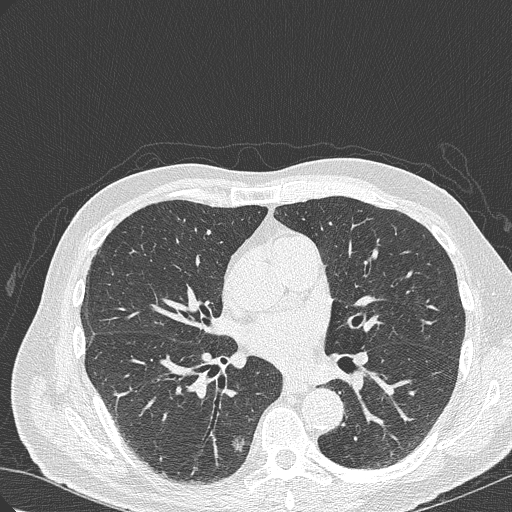
Chest CT (low-dose screening protocol), one axial image, first (baseline) screen, lung window (W 1500 / L -600 HU), 512 × 512 image matrix. Male, age 70 years at enrolment.
- Lesion marked by an expert reader, bounding box <197,420,260,483> (left, top, right, bottom; pixels).
- The screening reader recorded 4 non-calcified nodules or masses ≥4 mm on this exam (right lower lobe, right lower lobe, right upper lobe, right lower lobe); which of them this box marks is not recorded.
- Lung cancer was diagnosed 978 days after this screen: bronchiolo-alveolar adenocarcinoma, NOS, right lower lobe, poorly differentiated (G3), stage IB (AJCC 6th edition), 30 mm at pathology.